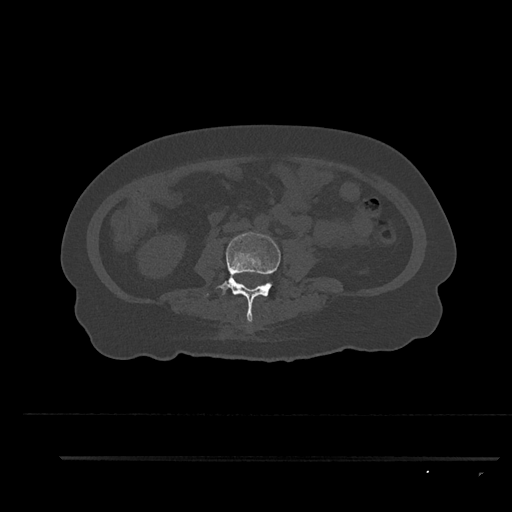
CT including the spine, one axial slice. Slice 81 of 797 in the series (ordered by position). Reconstruction kernel Br40s/3. 120 kVp. Bone window (W 1800 / L 400 HU). 0.5 mm slice thickness. 512 × 512 image matrix. Female patient, age 44 years. Case-level facts recorded for this patient, not image findings: primary cancer: renal; vertebrae with lytic lesions (as recorded): L1.
Structures marked on this image (semi-automatic segmentation, software-assisted and operator-edited):
- L3 vertebra: bounding box [x1, y1, x2, y2] px = [207, 231, 281, 323]